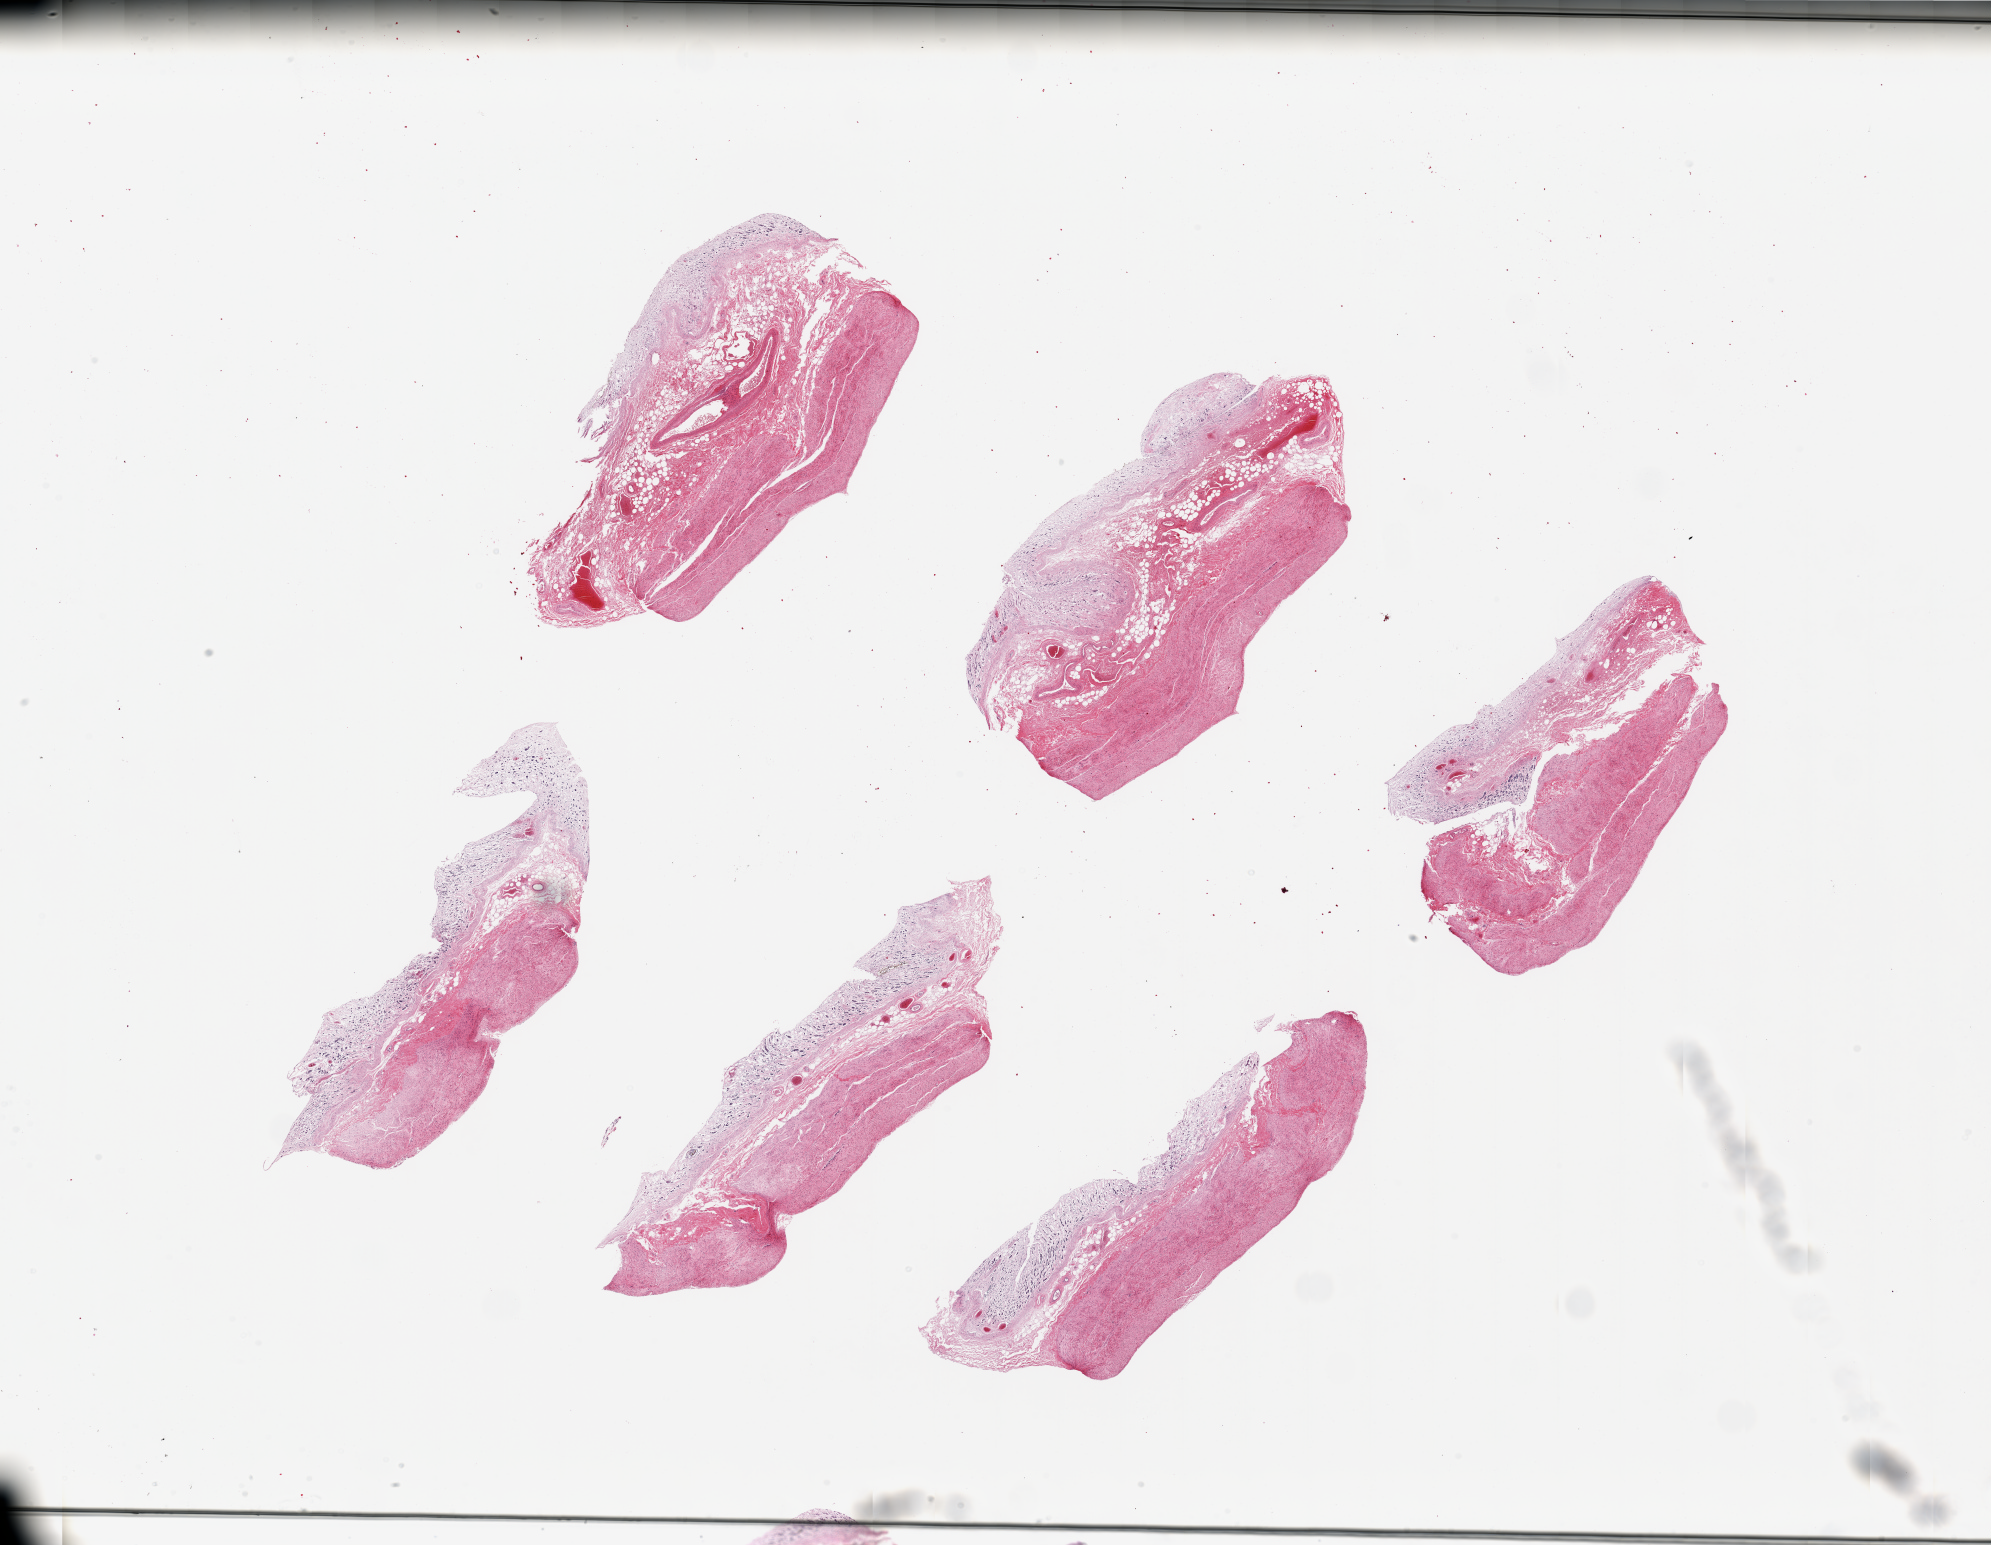
Digitized H&E-stained section, whole scanned area (about 31.5 x 24.4 mm, slide scanned at 20x) shown as a low-resolution overview, PAXgene-fixed paraffin-embedded (PFPE) section, section of stomach (target tissue), tissue donor sample. Donor sex: female.
- pathologist's review note for this sample: 6 pieces, up to 7x4mm; mucosa totally autolyzed; muscle not in good shape either